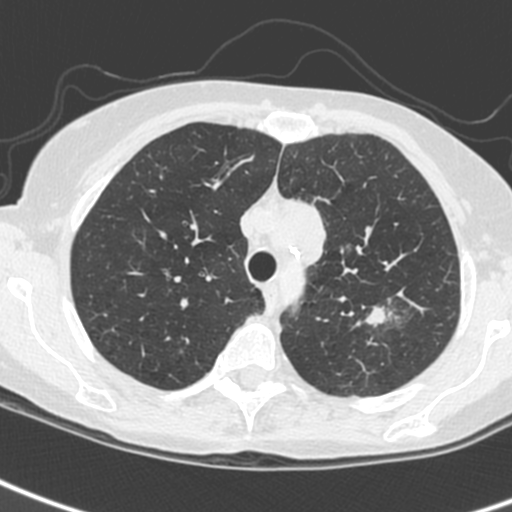
Low-dose screening chest CT, one axial slice; position 193 of 242 along the scan axis; lung window (W 1500 / L -600 HU); 1.3 mm slice thickness; 512 × 512 image matrix, field of view 284 × 284 mm.
Annotated regions visible in this slice (expert manual segmentation):
- lesion 1 (tumor, upper lobe of left lung): bounding box [x1, y1, x2, y2] px = [365, 307, 386, 325]
- lesion 3 (tumor, upper lobe of left lung): [293, 199, 326, 267]